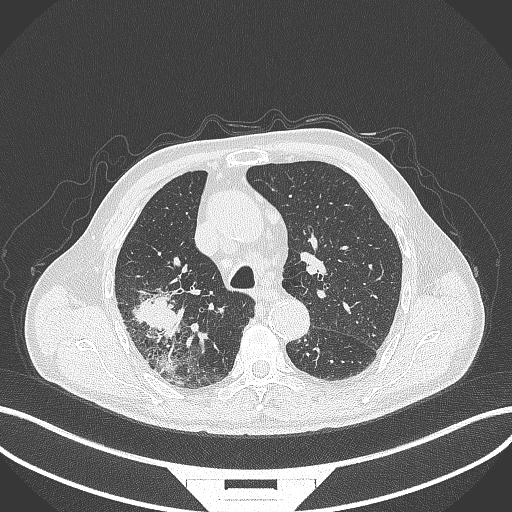
Chest CT, one axial slice; position 286 of 429 along the scan axis; reconstruction kernel B70f; 120 kVp; lung window (W 1500 / L -600 HU); 1 mm slice thickness; 512 × 512 image matrix. Male patient, age 72 years. From the clinical record (not read from this slice): clinical TNM (as recorded): T3 N2 M0.
Outlined on this slice (rectangle marked by the reading radiologist):
- lung tumour (recorded histology: adenocarcinoma): bounding box [x1, y1, x2, y2] px = [132, 289, 188, 341]